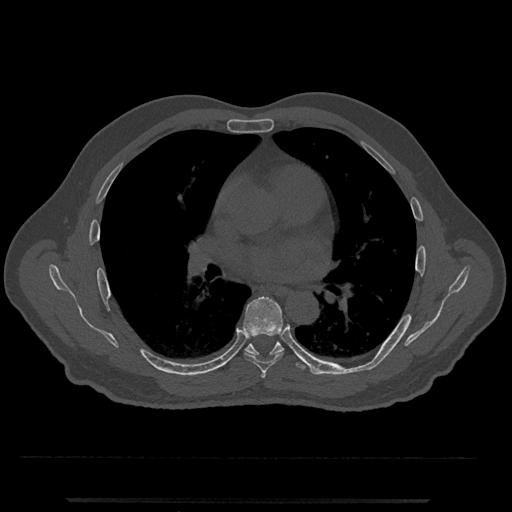
CT including the spine, one axial slice; reconstruction kernel Br40s/3; 120 kVp; bone window (W 1800 / L 400 HU); 512 × 512 image matrix, field of view 419 × 419 mm. Patient: male, 63 years. Case-level facts recorded for this patient, not image findings: primary cancer: prostate.
Annotated regions visible in this slice (semi-automatic segmentation, software-assisted and operator-edited):
- T5 vertebra: bounding box (x1, y1, x2, y2) in pixels: (261, 372, 266, 378)
- T6 vertebra: (243, 296, 283, 373)
- T7 vertebra: (245, 341, 320, 375)